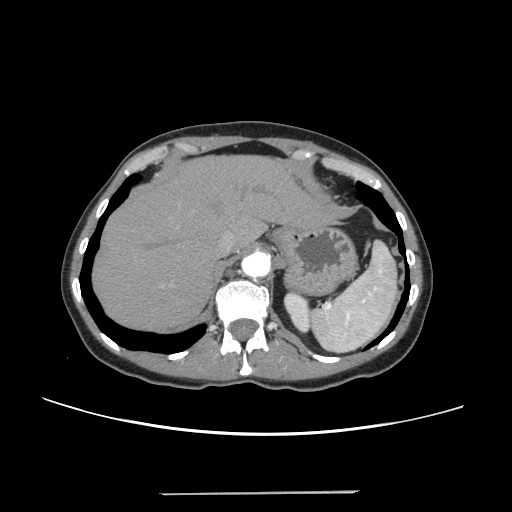
Contrast-enhanced abdominal CT, one axial slice. Position 196 of 240 along the scan axis. 120 kVp. Soft-tissue window (W 400 / L 40 HU). 512 × 512 image matrix, field of view 371 × 371 mm. Female patient, age 60 years. Case-level facts recorded for this patient, not image findings: diagnosis: colorectal cancer liver metastases, imaged before liver resection; multiple liver metastases: no; largest metastasis: 1.5 cm; disease in both lobes: no.
Annotated regions visible in this slice (expert manual segmentation):
- hepatic veins: bounding box (x1, y1, x2, y2) in pixels: (221, 233, 234, 252)
- liver: (94, 157, 327, 331)
- planned liver remnant (the part of the liver to remain after resection): (94, 157, 327, 331)